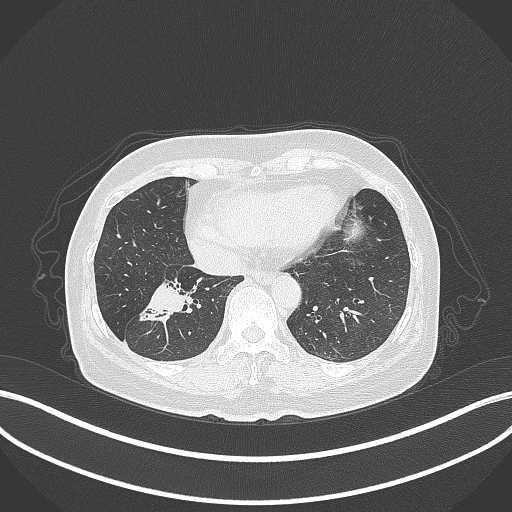
Chest CT, one axial slice; position 119 of 429 along the scan axis; reconstruction kernel B70f; 120 kVp; lung window (W 1500 / L -600 HU); 1 mm slice thickness; 512 × 512 image matrix, field of view 400 × 400 mm. Female patient, age 67 years. From the clinical record (not read from this slice): clinical TNM (as recorded): T1c N1 M0; histopathological grade: G2-3.
Annotated regions visible in this slice (rectangle marked by the reading radiologist):
- lung tumour (recorded histology: adenocarcinoma): bounding box [x1, y1, x2, y2] px = [139, 274, 189, 327]